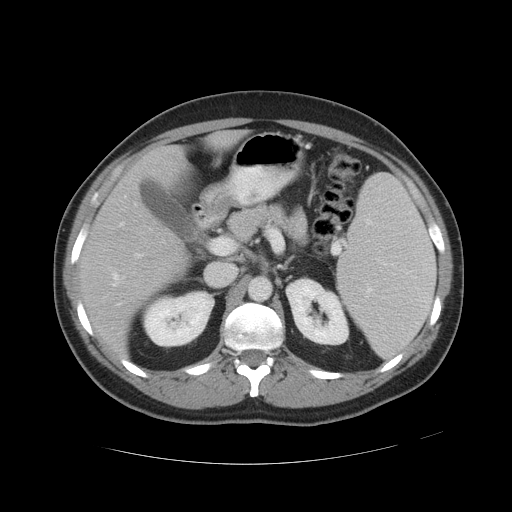
Contrast-enhanced abdominal CT, one axial slice. Reconstruction kernel STANDARD. 120 kVp. Intravenous contrast given. Soft-tissue window (W 400 / L 40 HU). 5 mm slice thickness. 512 × 512 image matrix, field of view 422 × 422 mm. Male patient, age 42 years. From the clinical record (not read from this slice): diagnosis: colorectal cancer liver metastases, imaged before liver resection; multiple liver metastases: yes; largest metastasis: 2.8 cm; disease in both lobes: yes.
Outlined on this slice (outlined manually by an expert reader):
- hepatic veins: bounding box <113,196,137,286> (left, top, right, bottom; pixels)
- liver: <82,135,234,352>
- planned liver remnant (the part of the liver to remain after resection): <82,135,234,351>
- portal vein (with intrahepatic branches): <136,254,142,258>